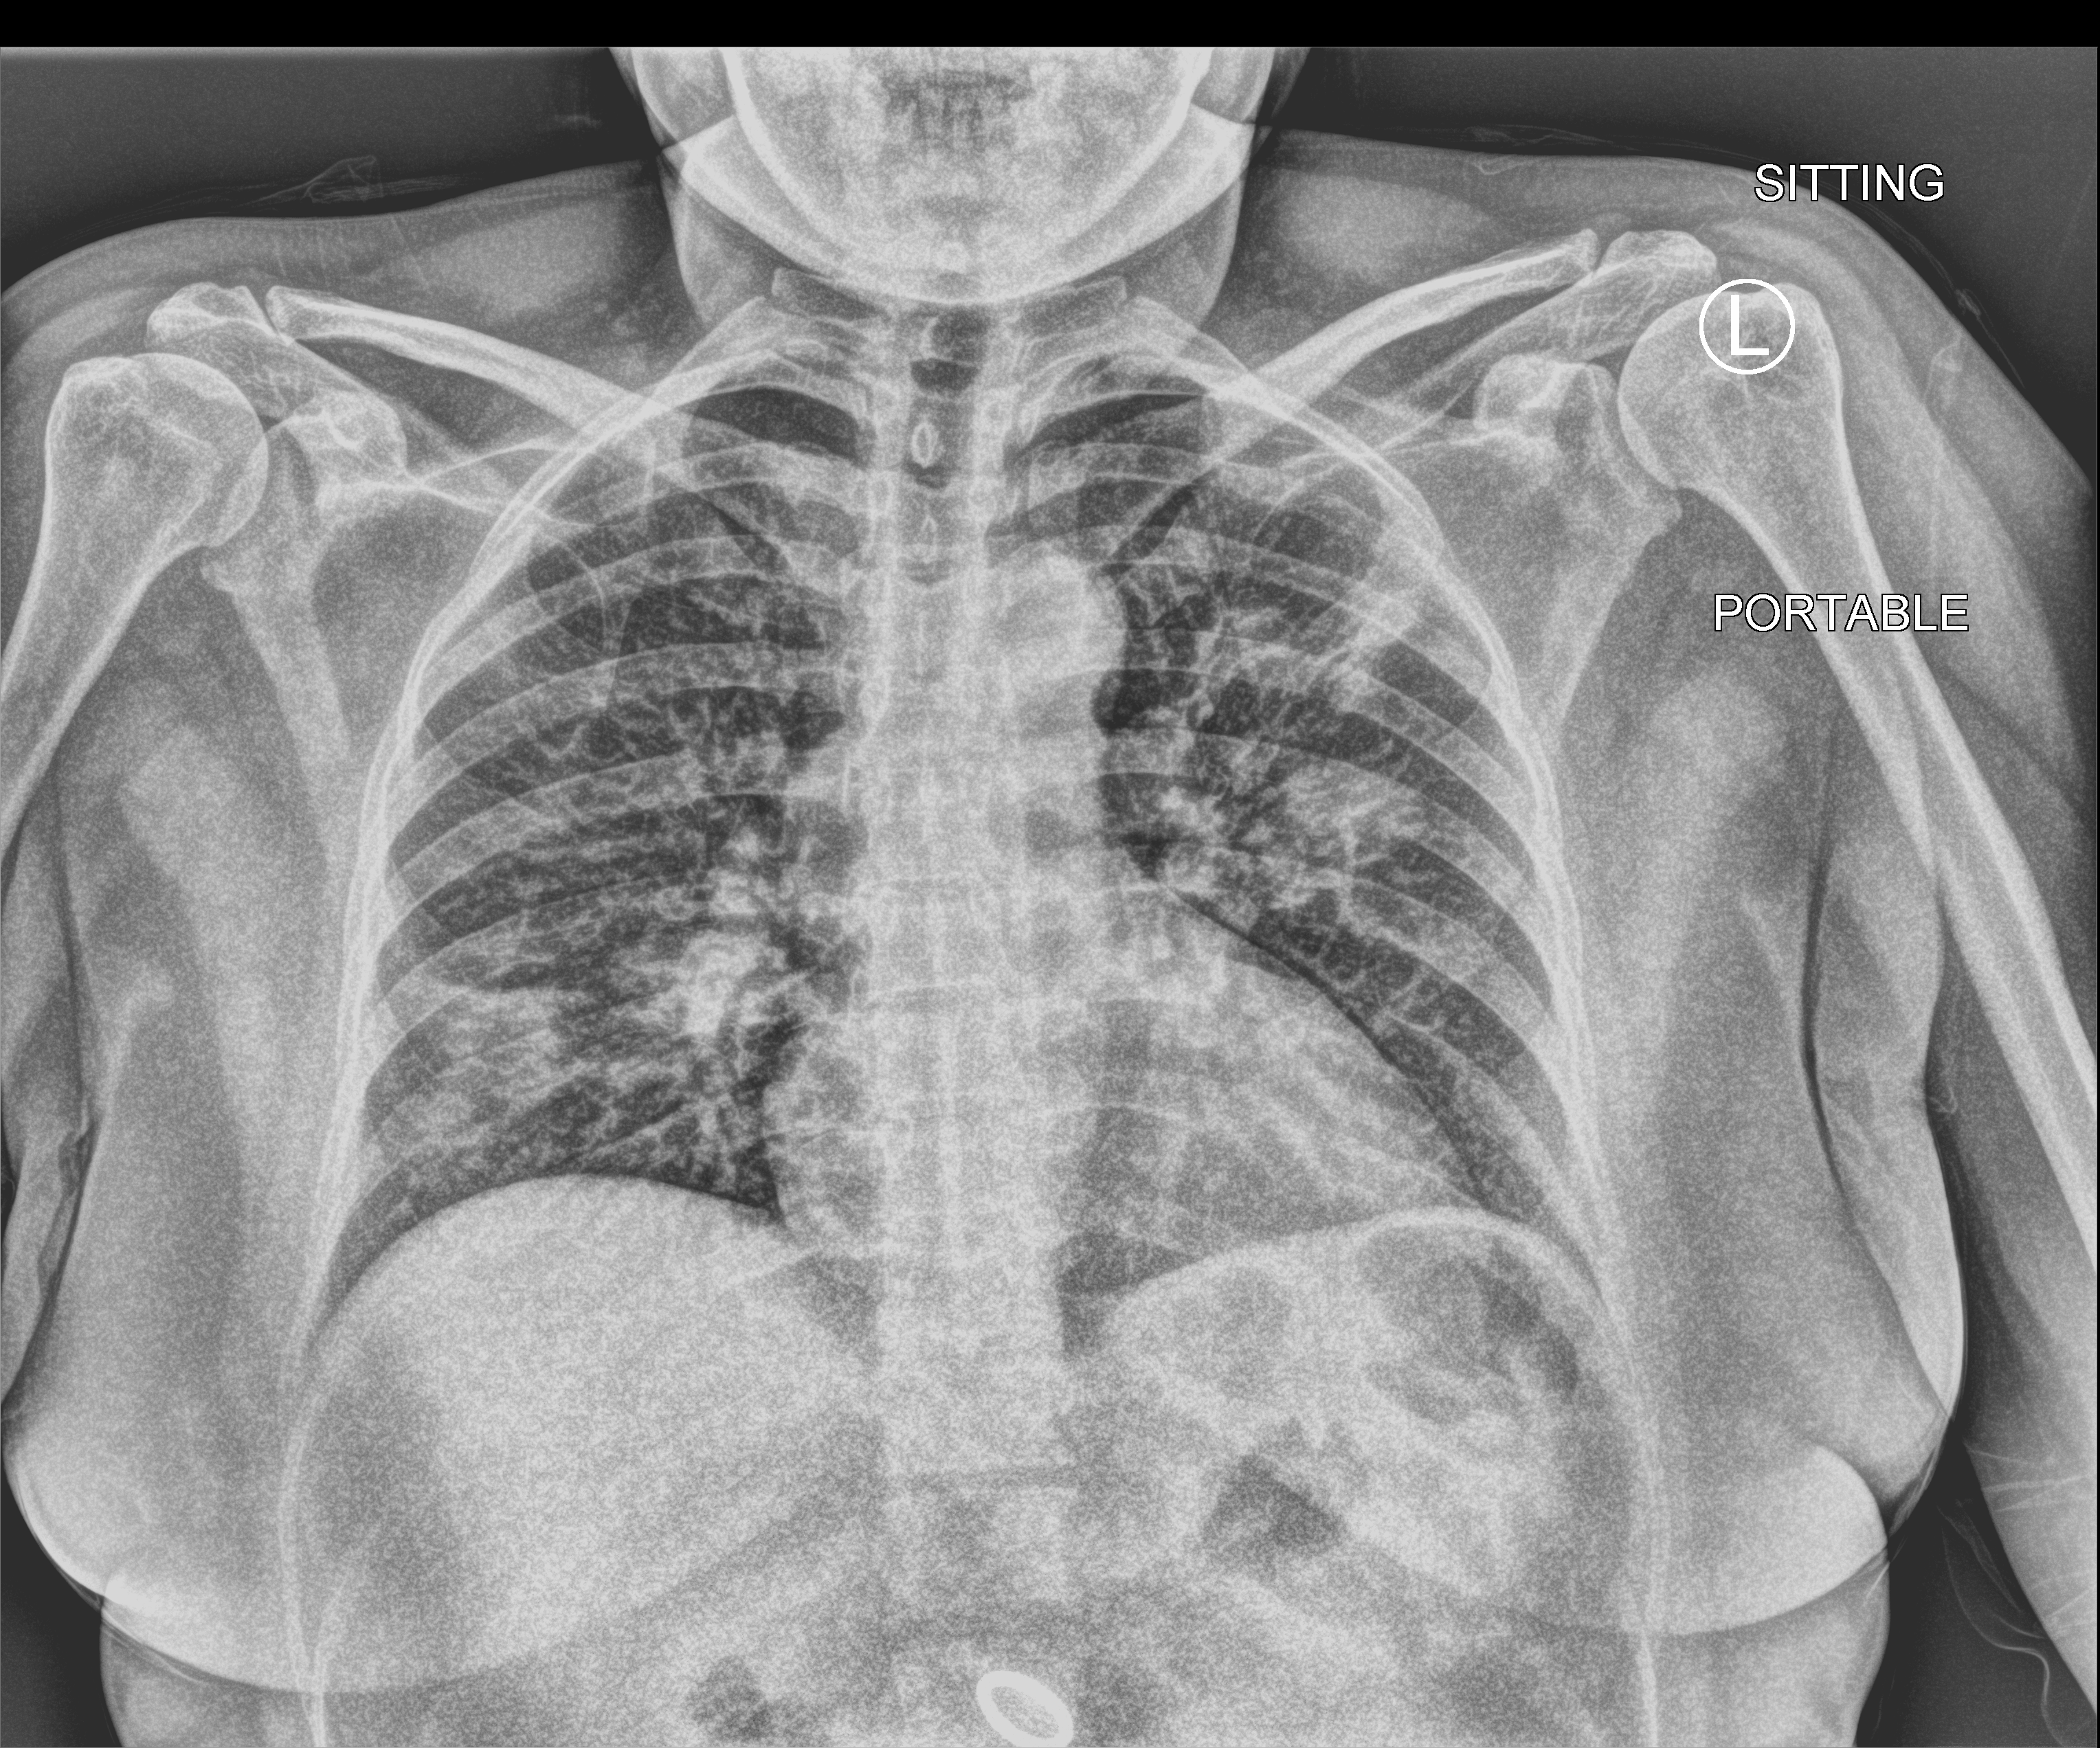
Chest X-ray (portable), anteroposterior (AP) projection. Patient hospitalised with COVID-19; female, aged 18–59 years.
From the hospital-stay record, not from the radiograph (when in the stay this image was taken is not recorded): mechanically ventilated during this hospital stay: no.